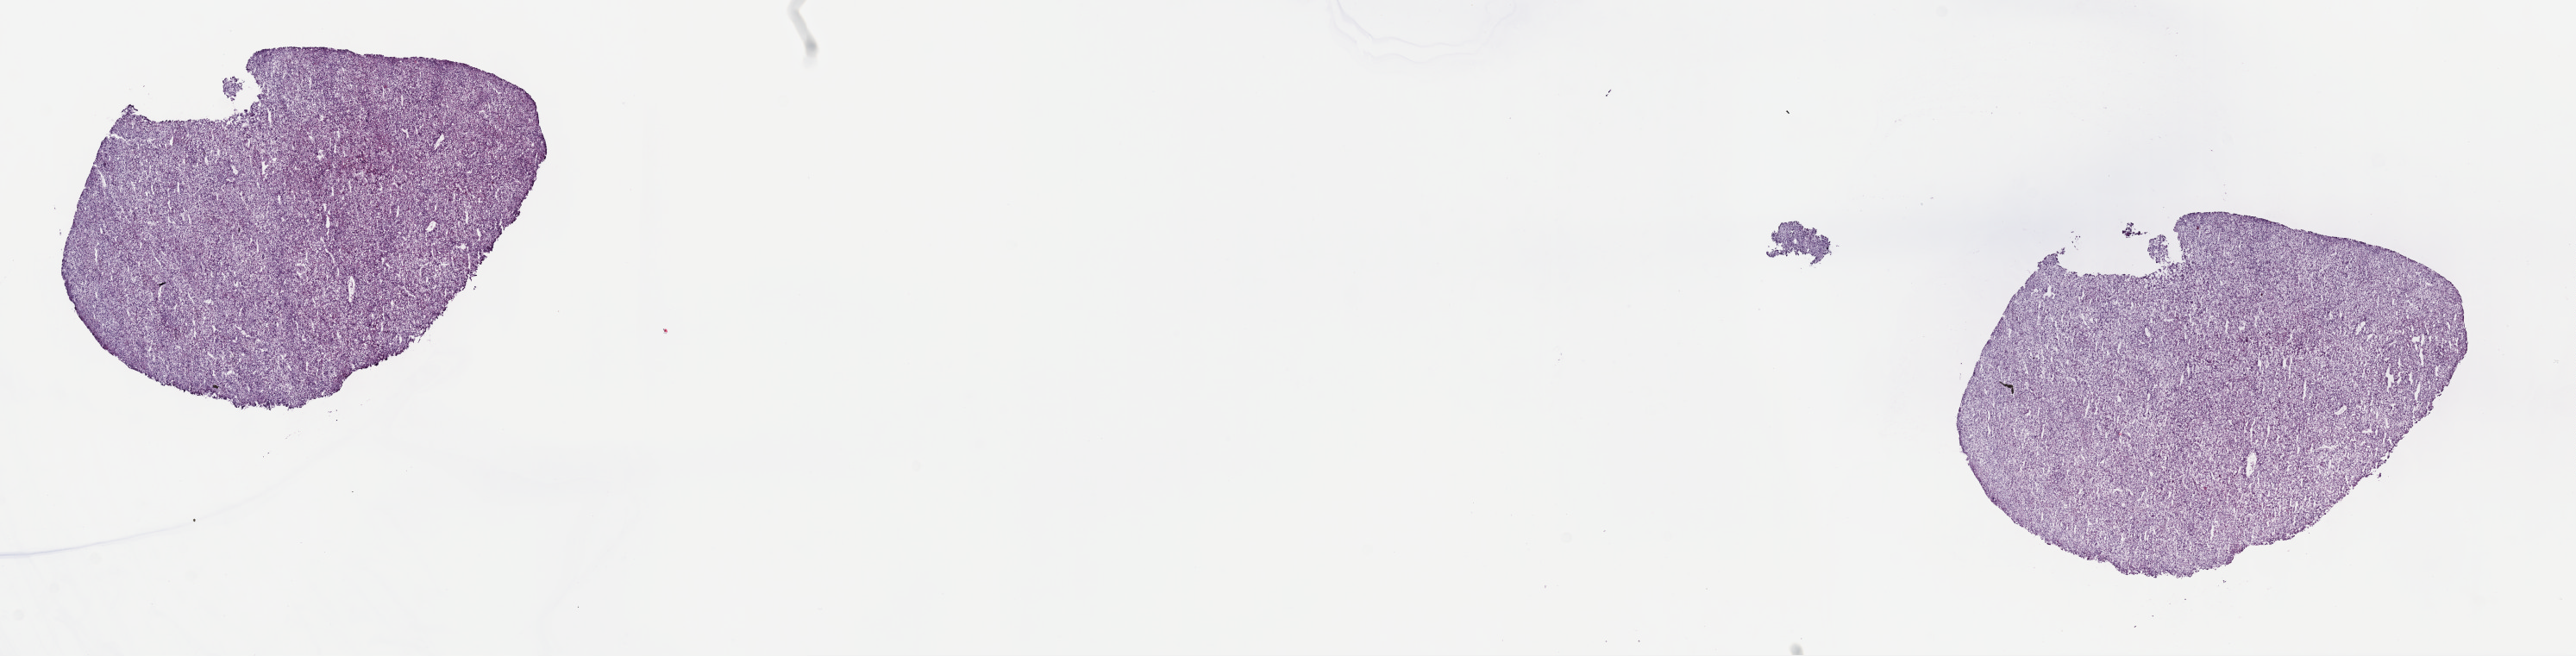
Whole-slide histology image, Hematoxylin and eosin (H&E) stained, low-resolution overview of the scanned area, about 24.2 x 6.2 mm (acquisition: 40x scan), frozen section from the top of the tissue portion, sample: primary tumour, liver. Male patient; age at initial diagnosis 66 years.
Diagnosis: Hepatocellular carcinoma, NOS.